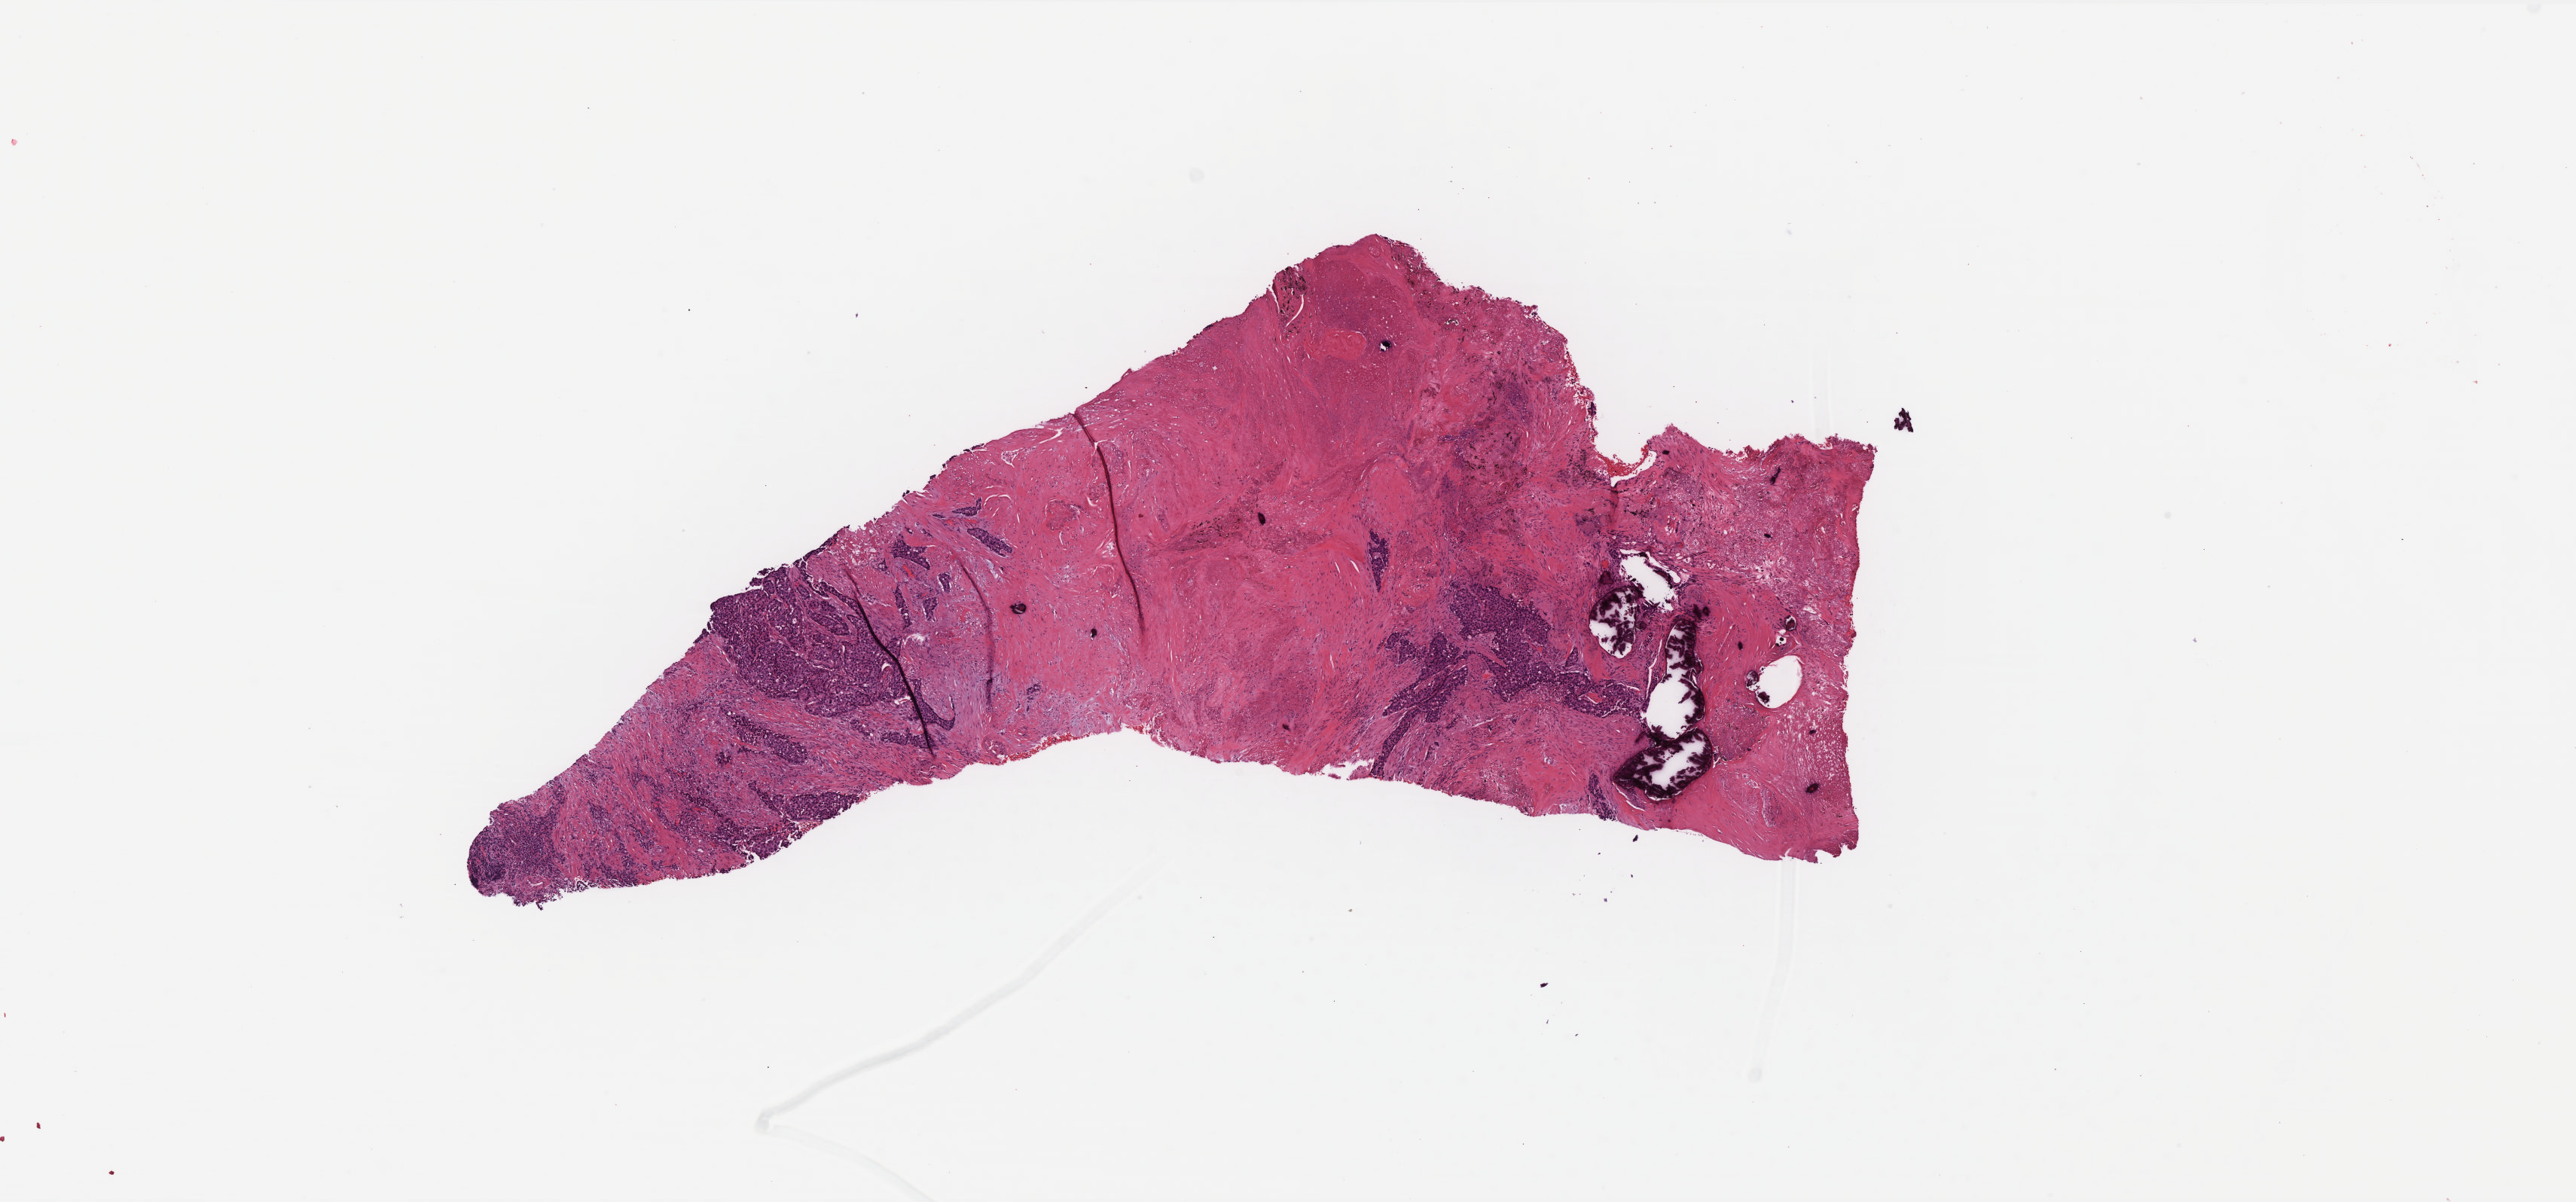
H&E whole-slide image — a low-resolution overview of the entire scanned area, about 13.7 x 6.4 mm; FFPE section; primary tumour sample from the lung. Male, age 73 years at initial diagnosis.
AJCC pathologic stage: IIB (7th edition). Laterality: right. TNM: T3 N0 M0. Histologic diagnosis: Adenocarcinoma, NOS.